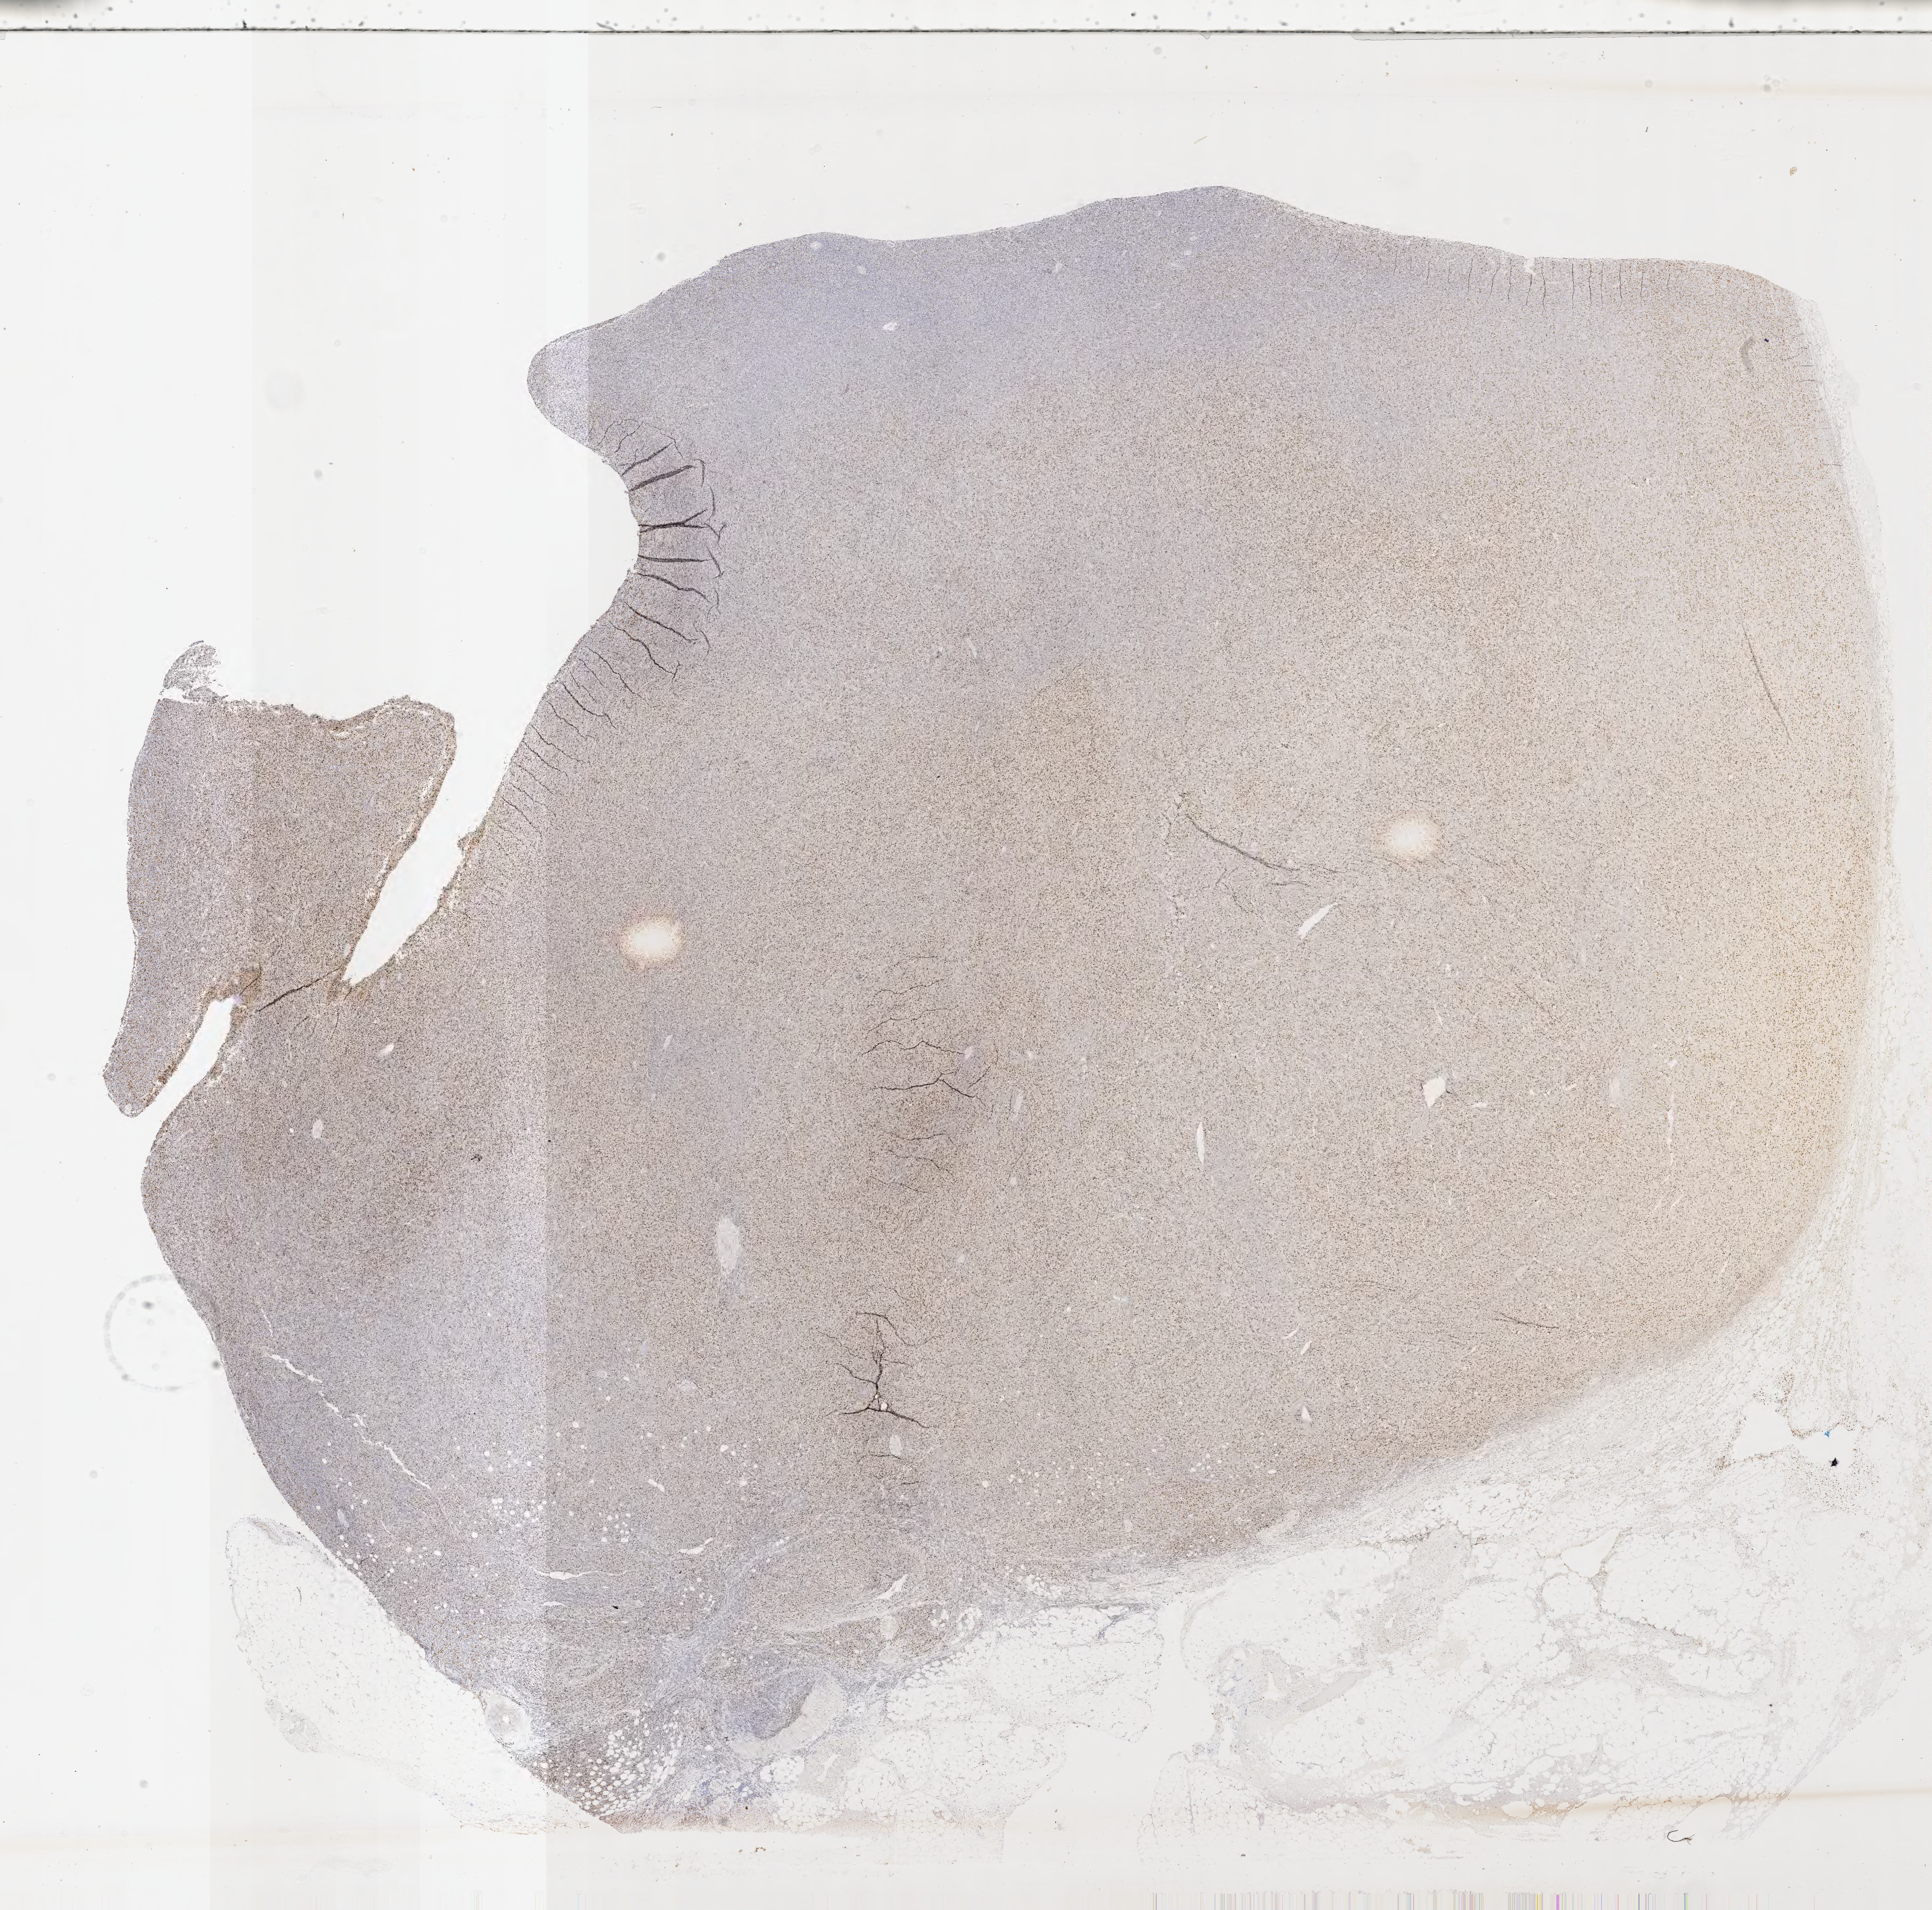
Whole-slide image, immunohistochemical stain for BCL6, shown as a low-resolution overview of the whole scanned area (about 23.1 x 22.9 mm); tumor tissue; site: lymph node. Patient: male, aged 54.
• diagnosis: Diffuse large B-cell lymphoma, NOS